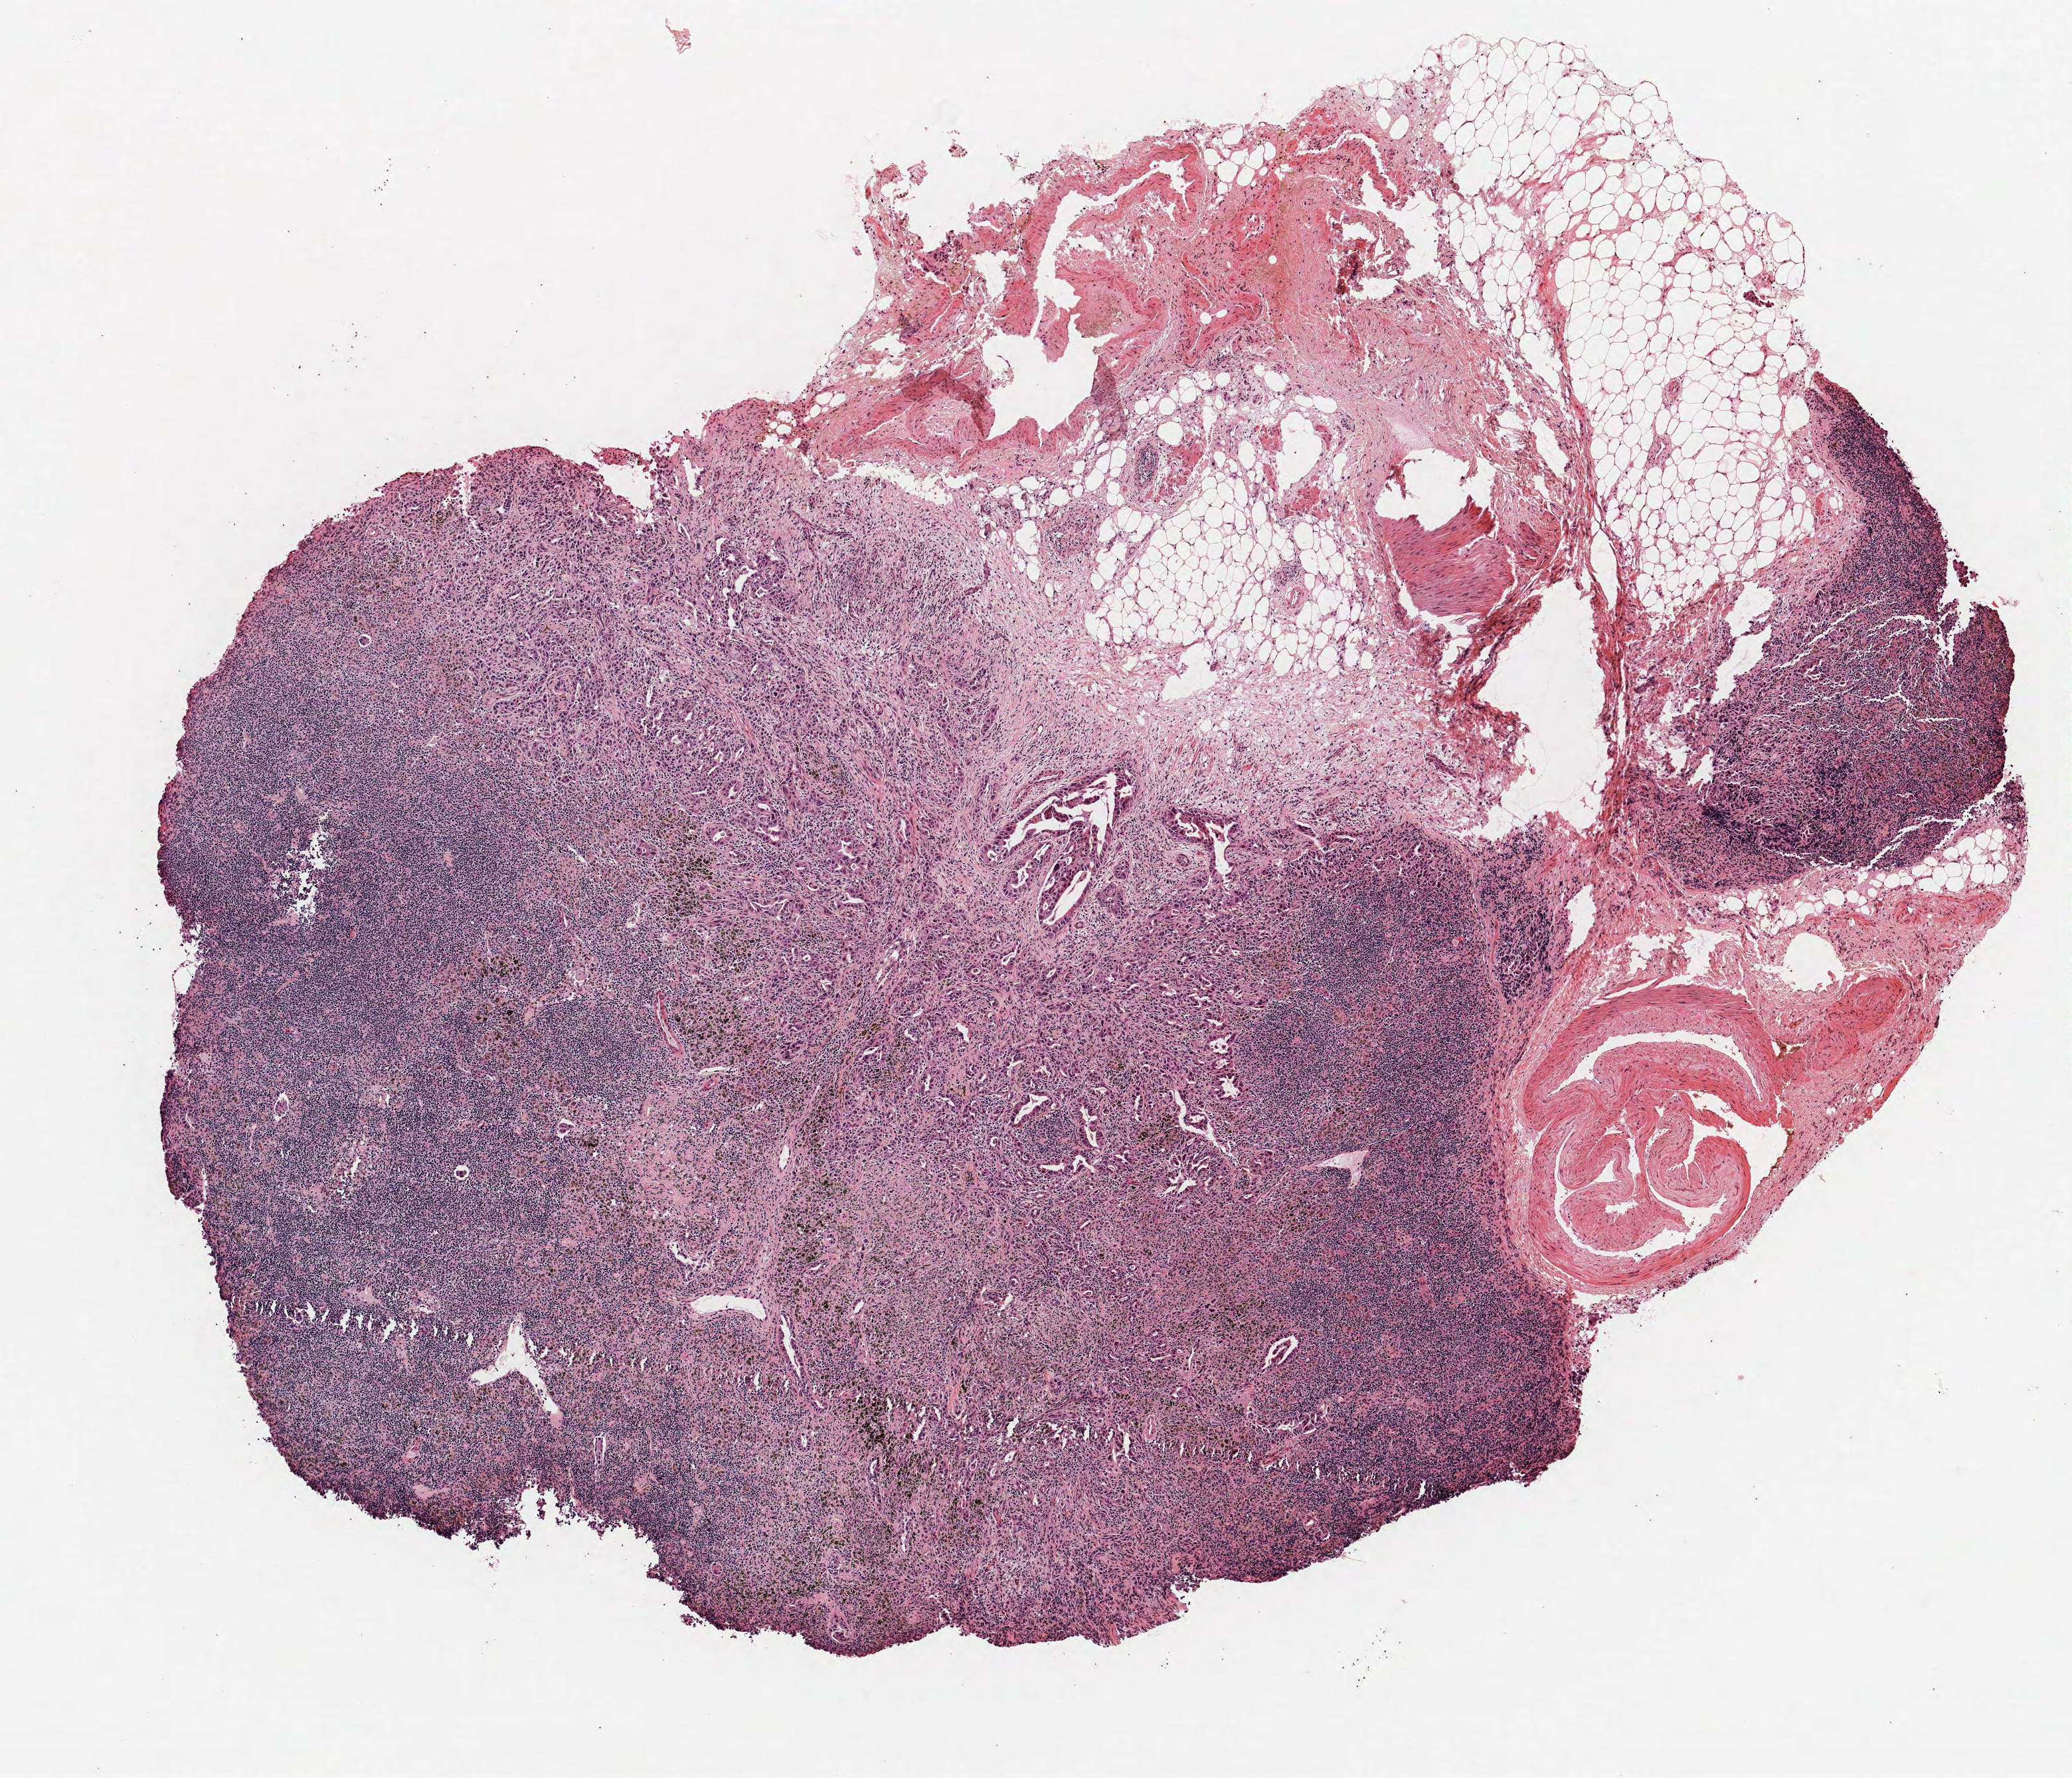
H&E whole-slide image, a low-resolution overview of the entire scanned area, about 6.2 x 5.4 mm (from a 40x scan). FFPE section. Lung tissue. Male, age 67 at enrolment. Current smoker at enrolment. Grade: cannot be assessed (GX).
Tumour size (pathology): 32 mm. Participant's lung-cancer diagnosis: Adenocarcinoma, NOS (ICD-O-3 8140/3). Primary tumour location (clinical record): right lower lobe. Stage (AJCC 6th edition): IIIB.